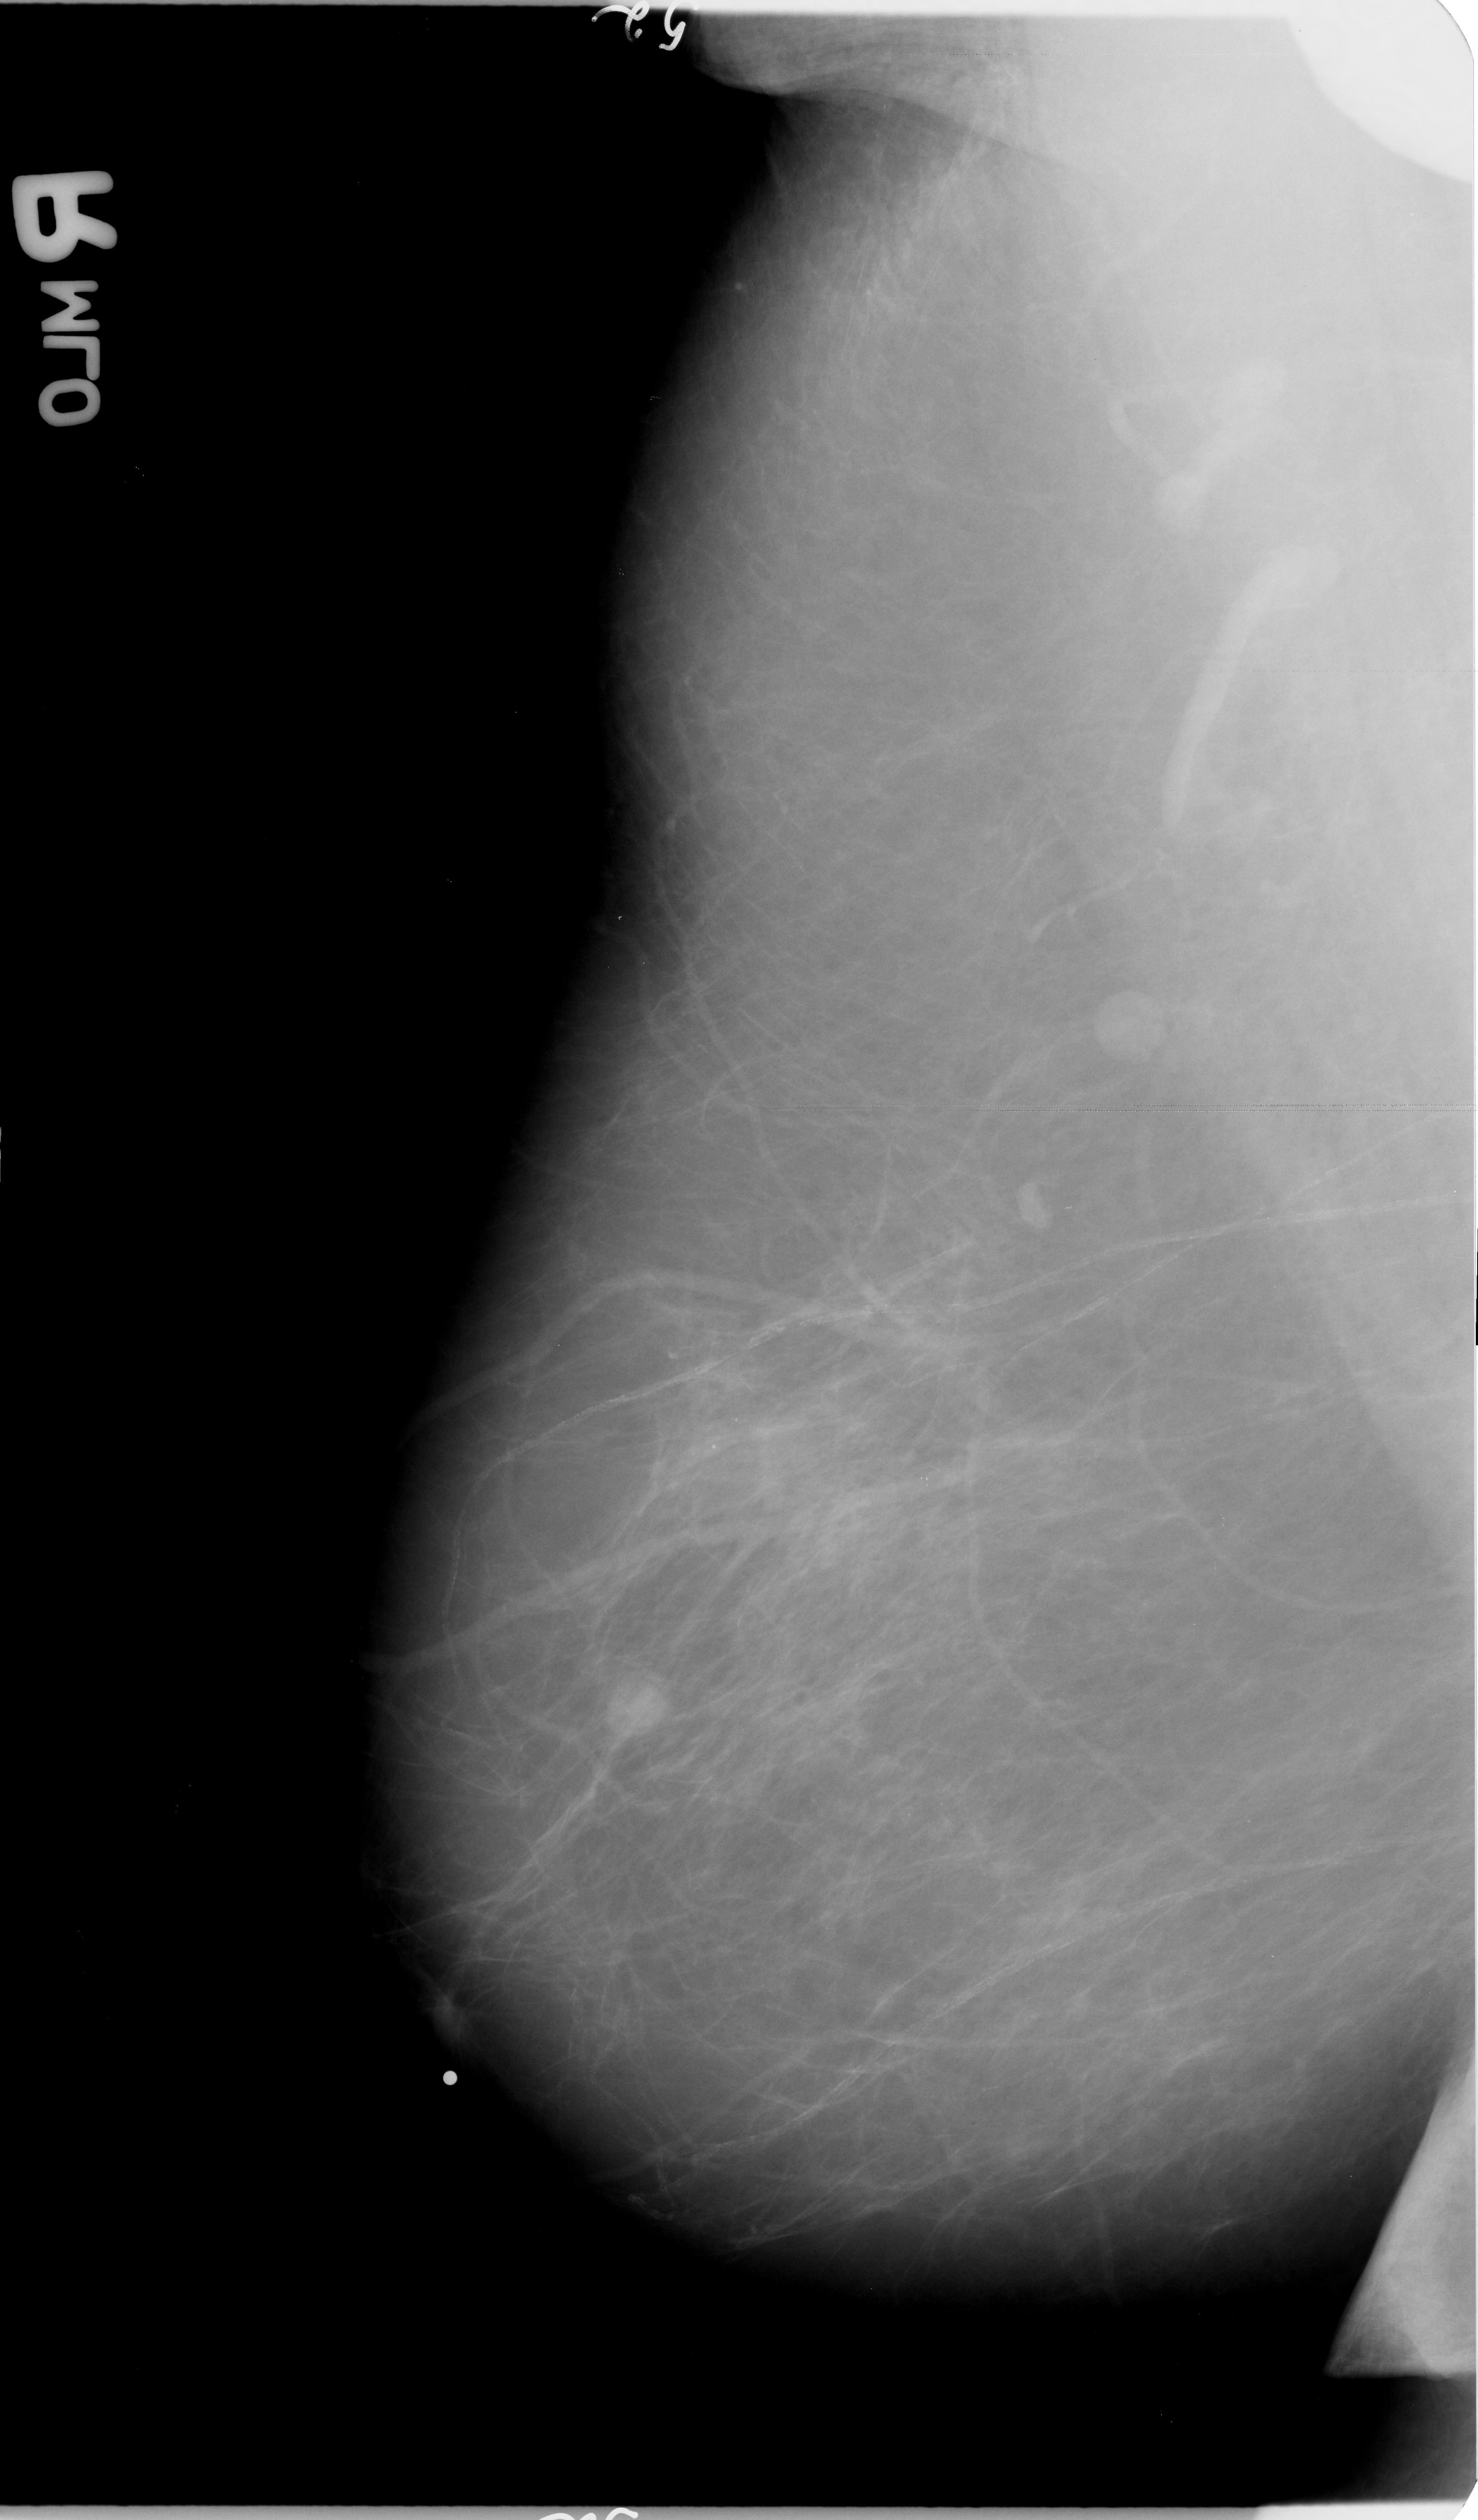
Mammogram (digitized film); right breast; MLO view; BI-RADS breast density category 1 (scale 1–4); 1478 × 2520 image matrix.
Marked abnormalities (boxes around the expert regions of interest):
- mass, shape irregular, margins ill defined; BI-RADS assessment category 3; subtlety rating 2 on a 1 (subtle) to 5 (obvious) scale; pathology (as recorded): malignant: bounding box <418,1970,497,2060> (left, top, right, bottom; pixels)